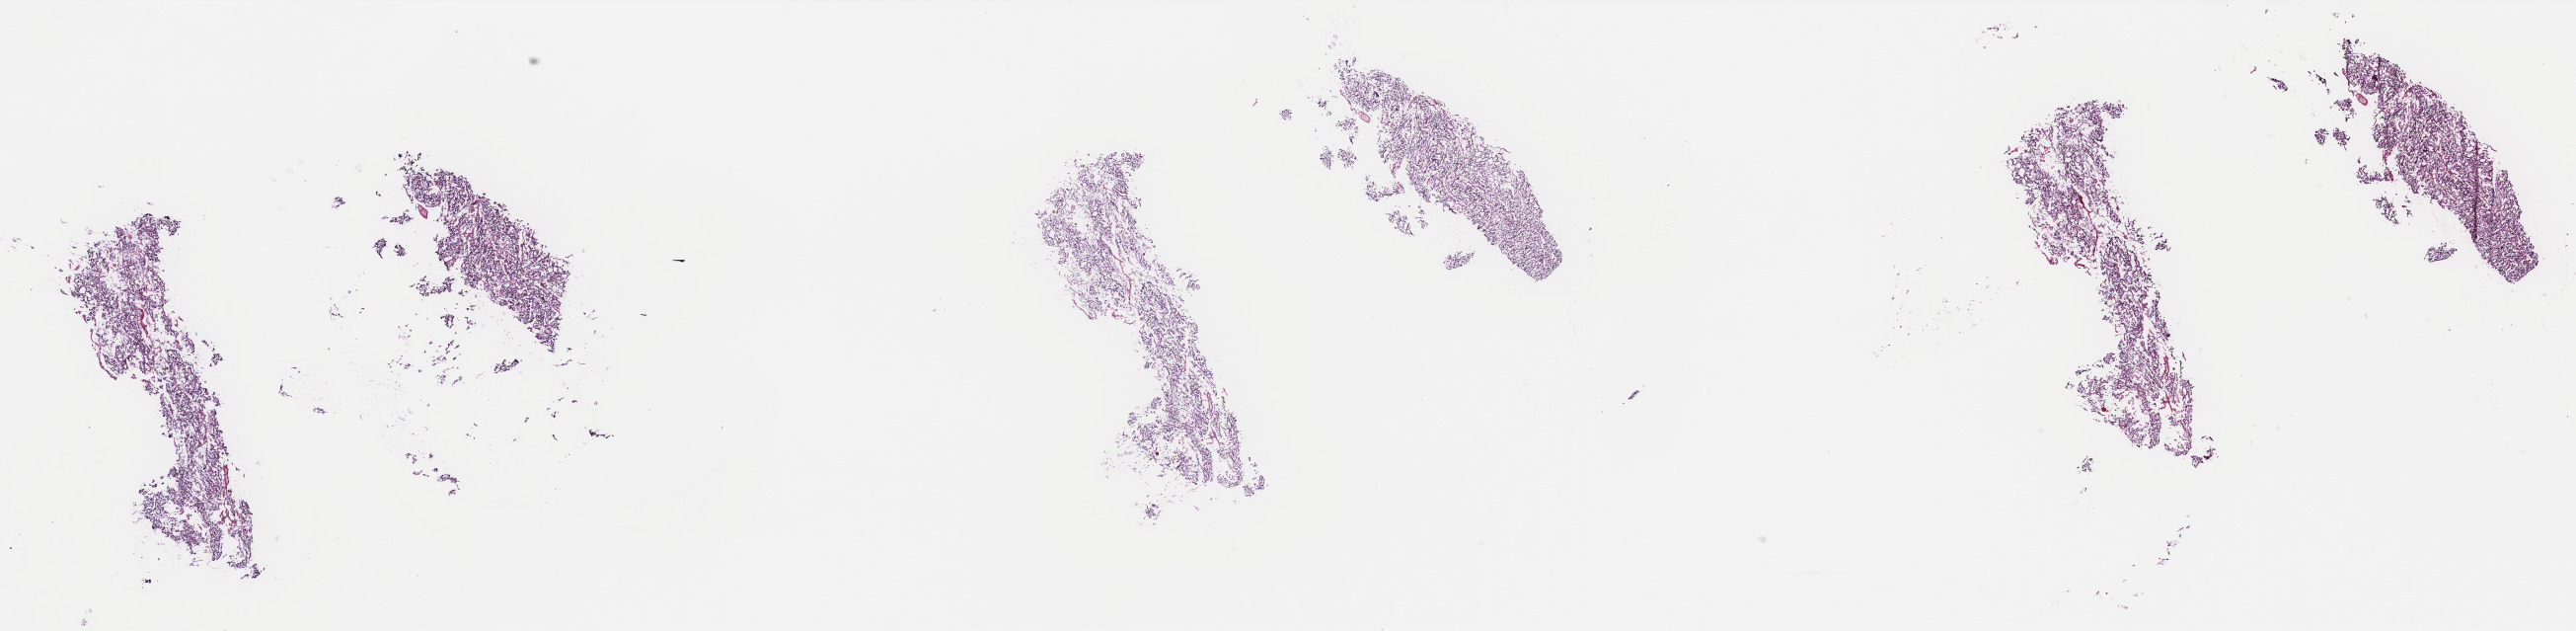
Whole-slide histology image, H&E-stained — low-resolution overview of the scanned area, about 41.8 x 10.2 mm; frozen section from the top of the tissue portion; kidney, primary tumour sample. Female, age 61 years at initial diagnosis. Pathologist review of this section (percent, as recorded): tumour cells 90%, tumour nuclei 95%, normal cells 0%, stromal cells 5%, necrosis 5%. Infiltration values recorded for this section: lymphocyte infiltration 0%, monocyte infiltration 0%, neutrophil infiltration 0%.
Histologic diagnosis: Renal cell carcinoma, chromophobe type. Laterality: right. TNM: T1a NX. AJCC pathologic stage: I.